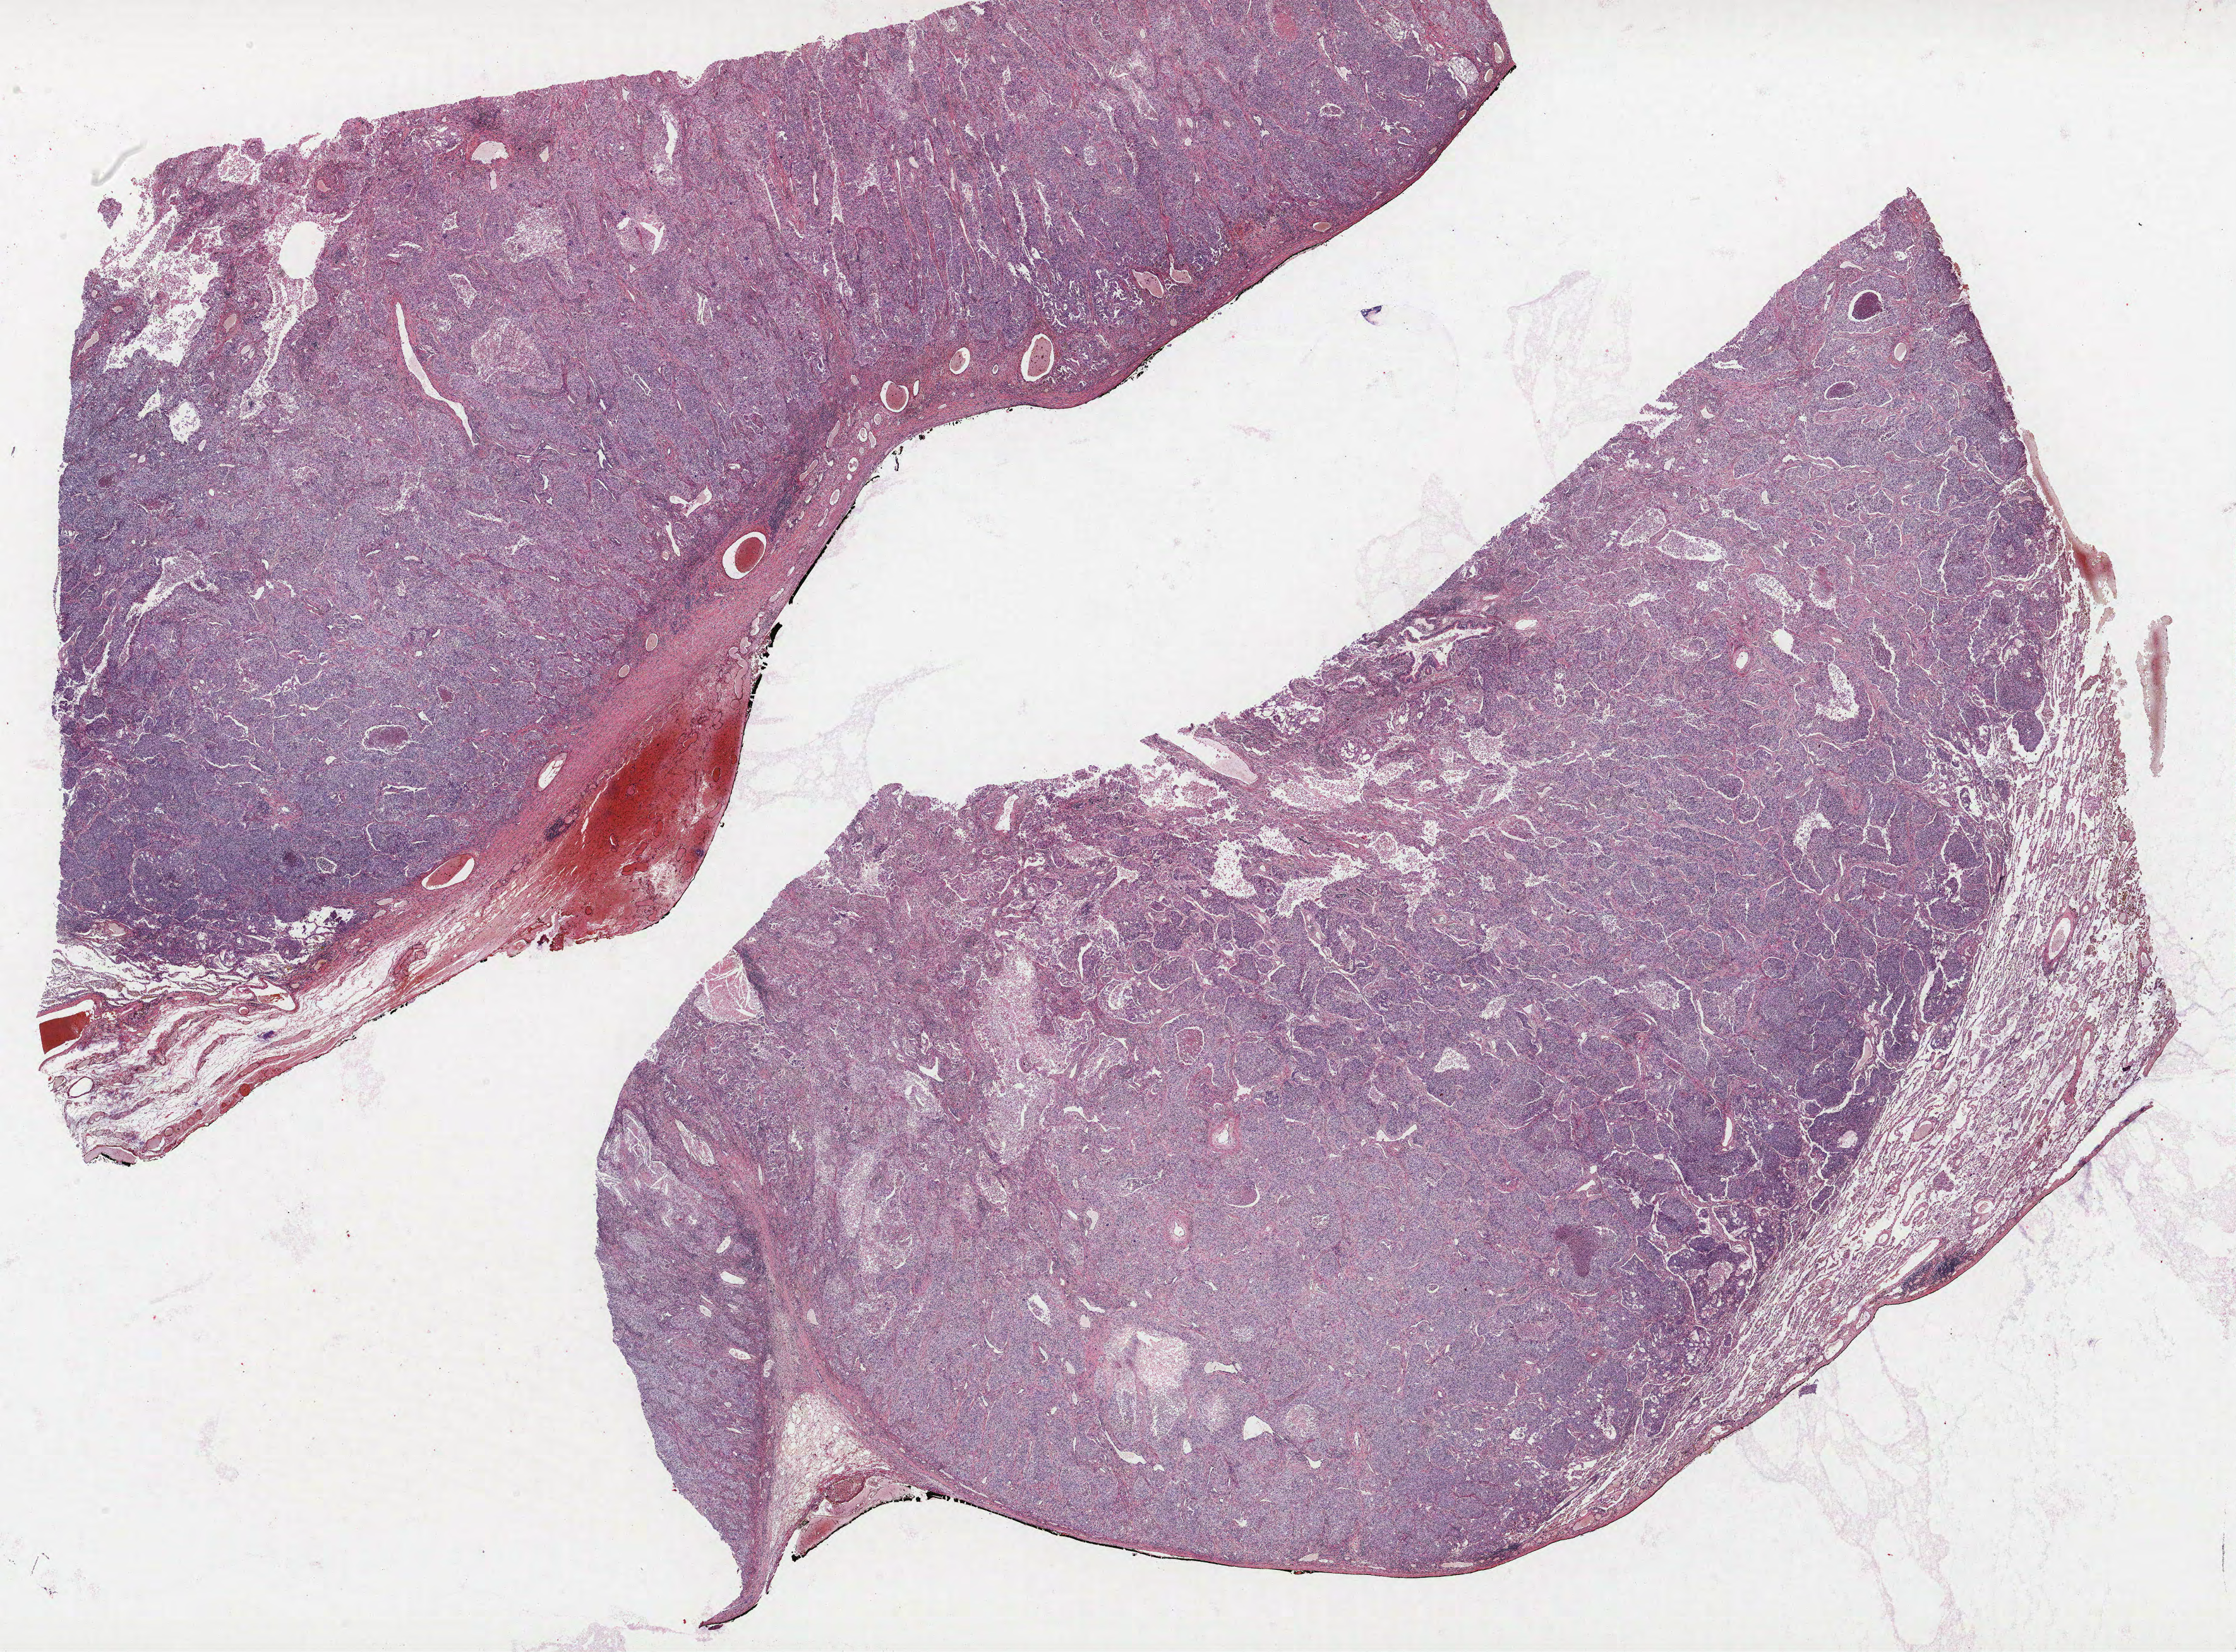
Whole-slide histology image, H&E-stained, a low-resolution overview of the entire scanned area, about 28.3 x 20.9 mm. FFPE section. Lung tissue. Male patient, aged 56 at enrolment. Current smoker at enrolment.
Participant's lung-cancer diagnosis: Adenocarcinoma, NOS.